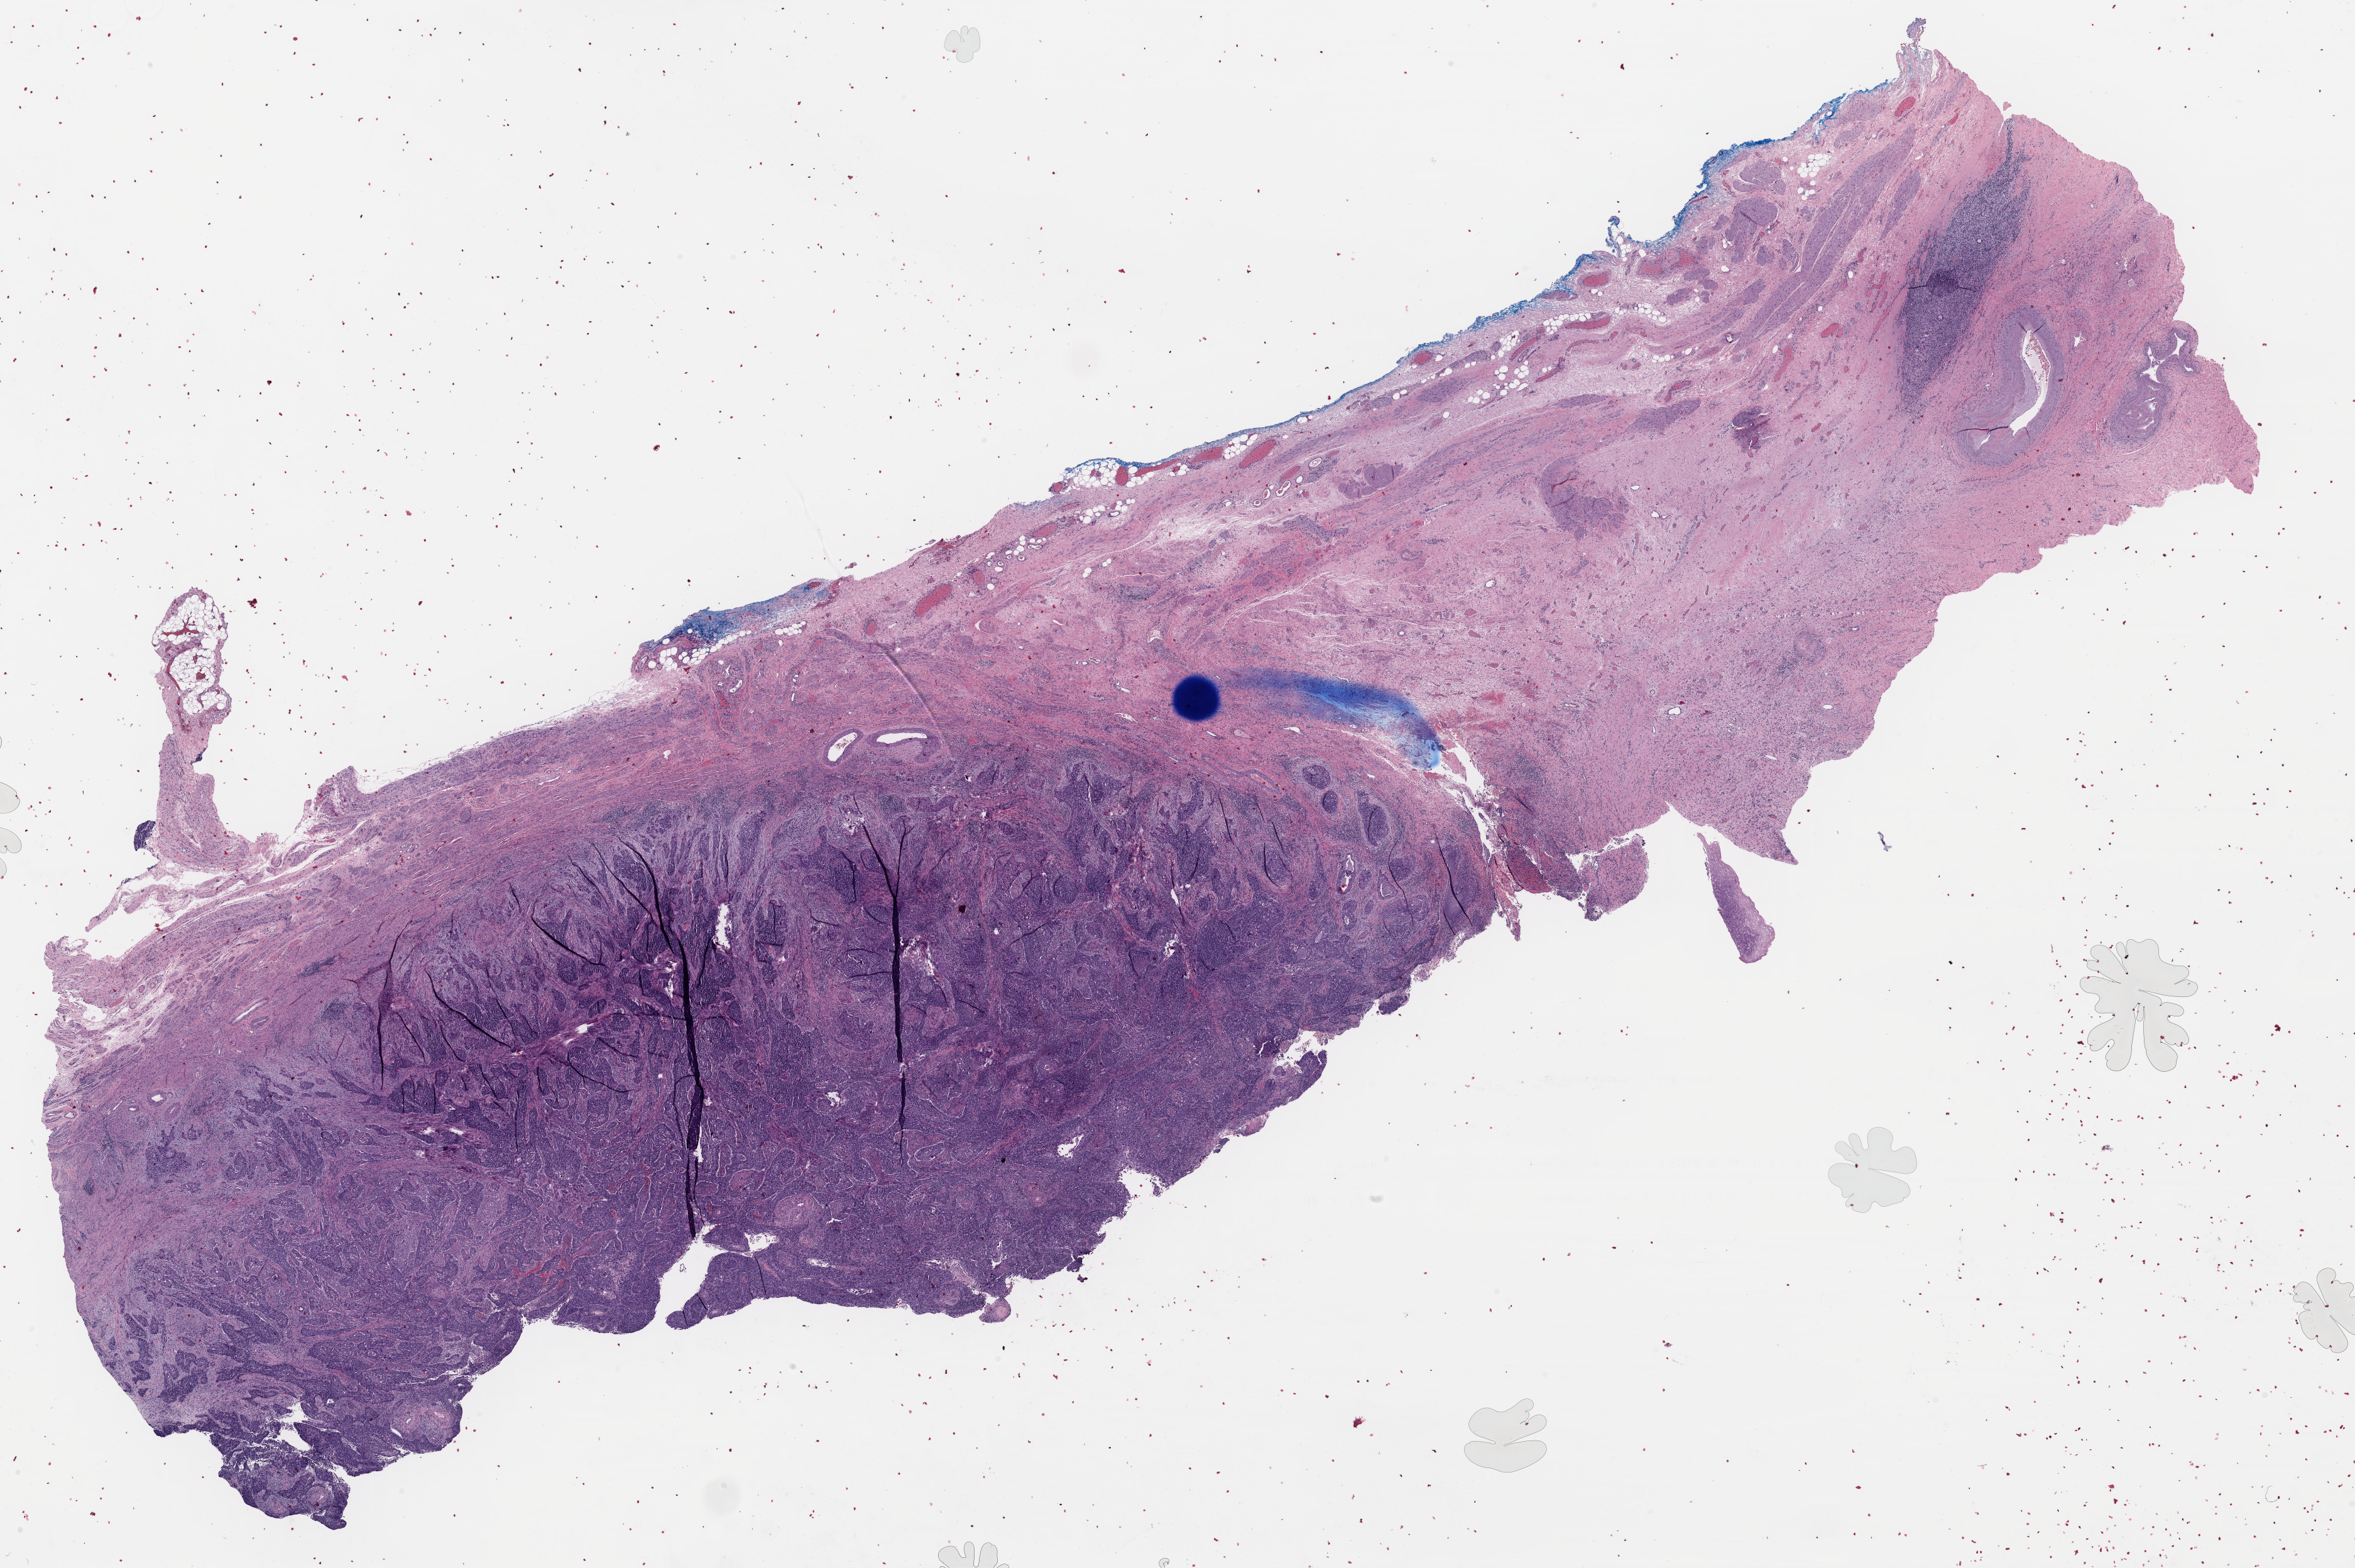
Digitized H&E tissue section (whole slide), whole scanned area (about 29.6 x 19.7 mm, slide scanned at 40x) shown as a low-resolution overview, formalin-fixed paraffin-embedded (FFPE) diagnostic section, sample: primary tumour, cervix. Female, age 49 years at initial diagnosis. Histologic grade: G3 (poorly differentiated).
Lymph nodes positive (case pathology): 0 of 6 examined. AJCC pathologic stage: IB1 (7th edition). Pathologic diagnosis: Squamous cell carcinoma, NOS (cervix uteri). TNM: T1b1 N0 M0.